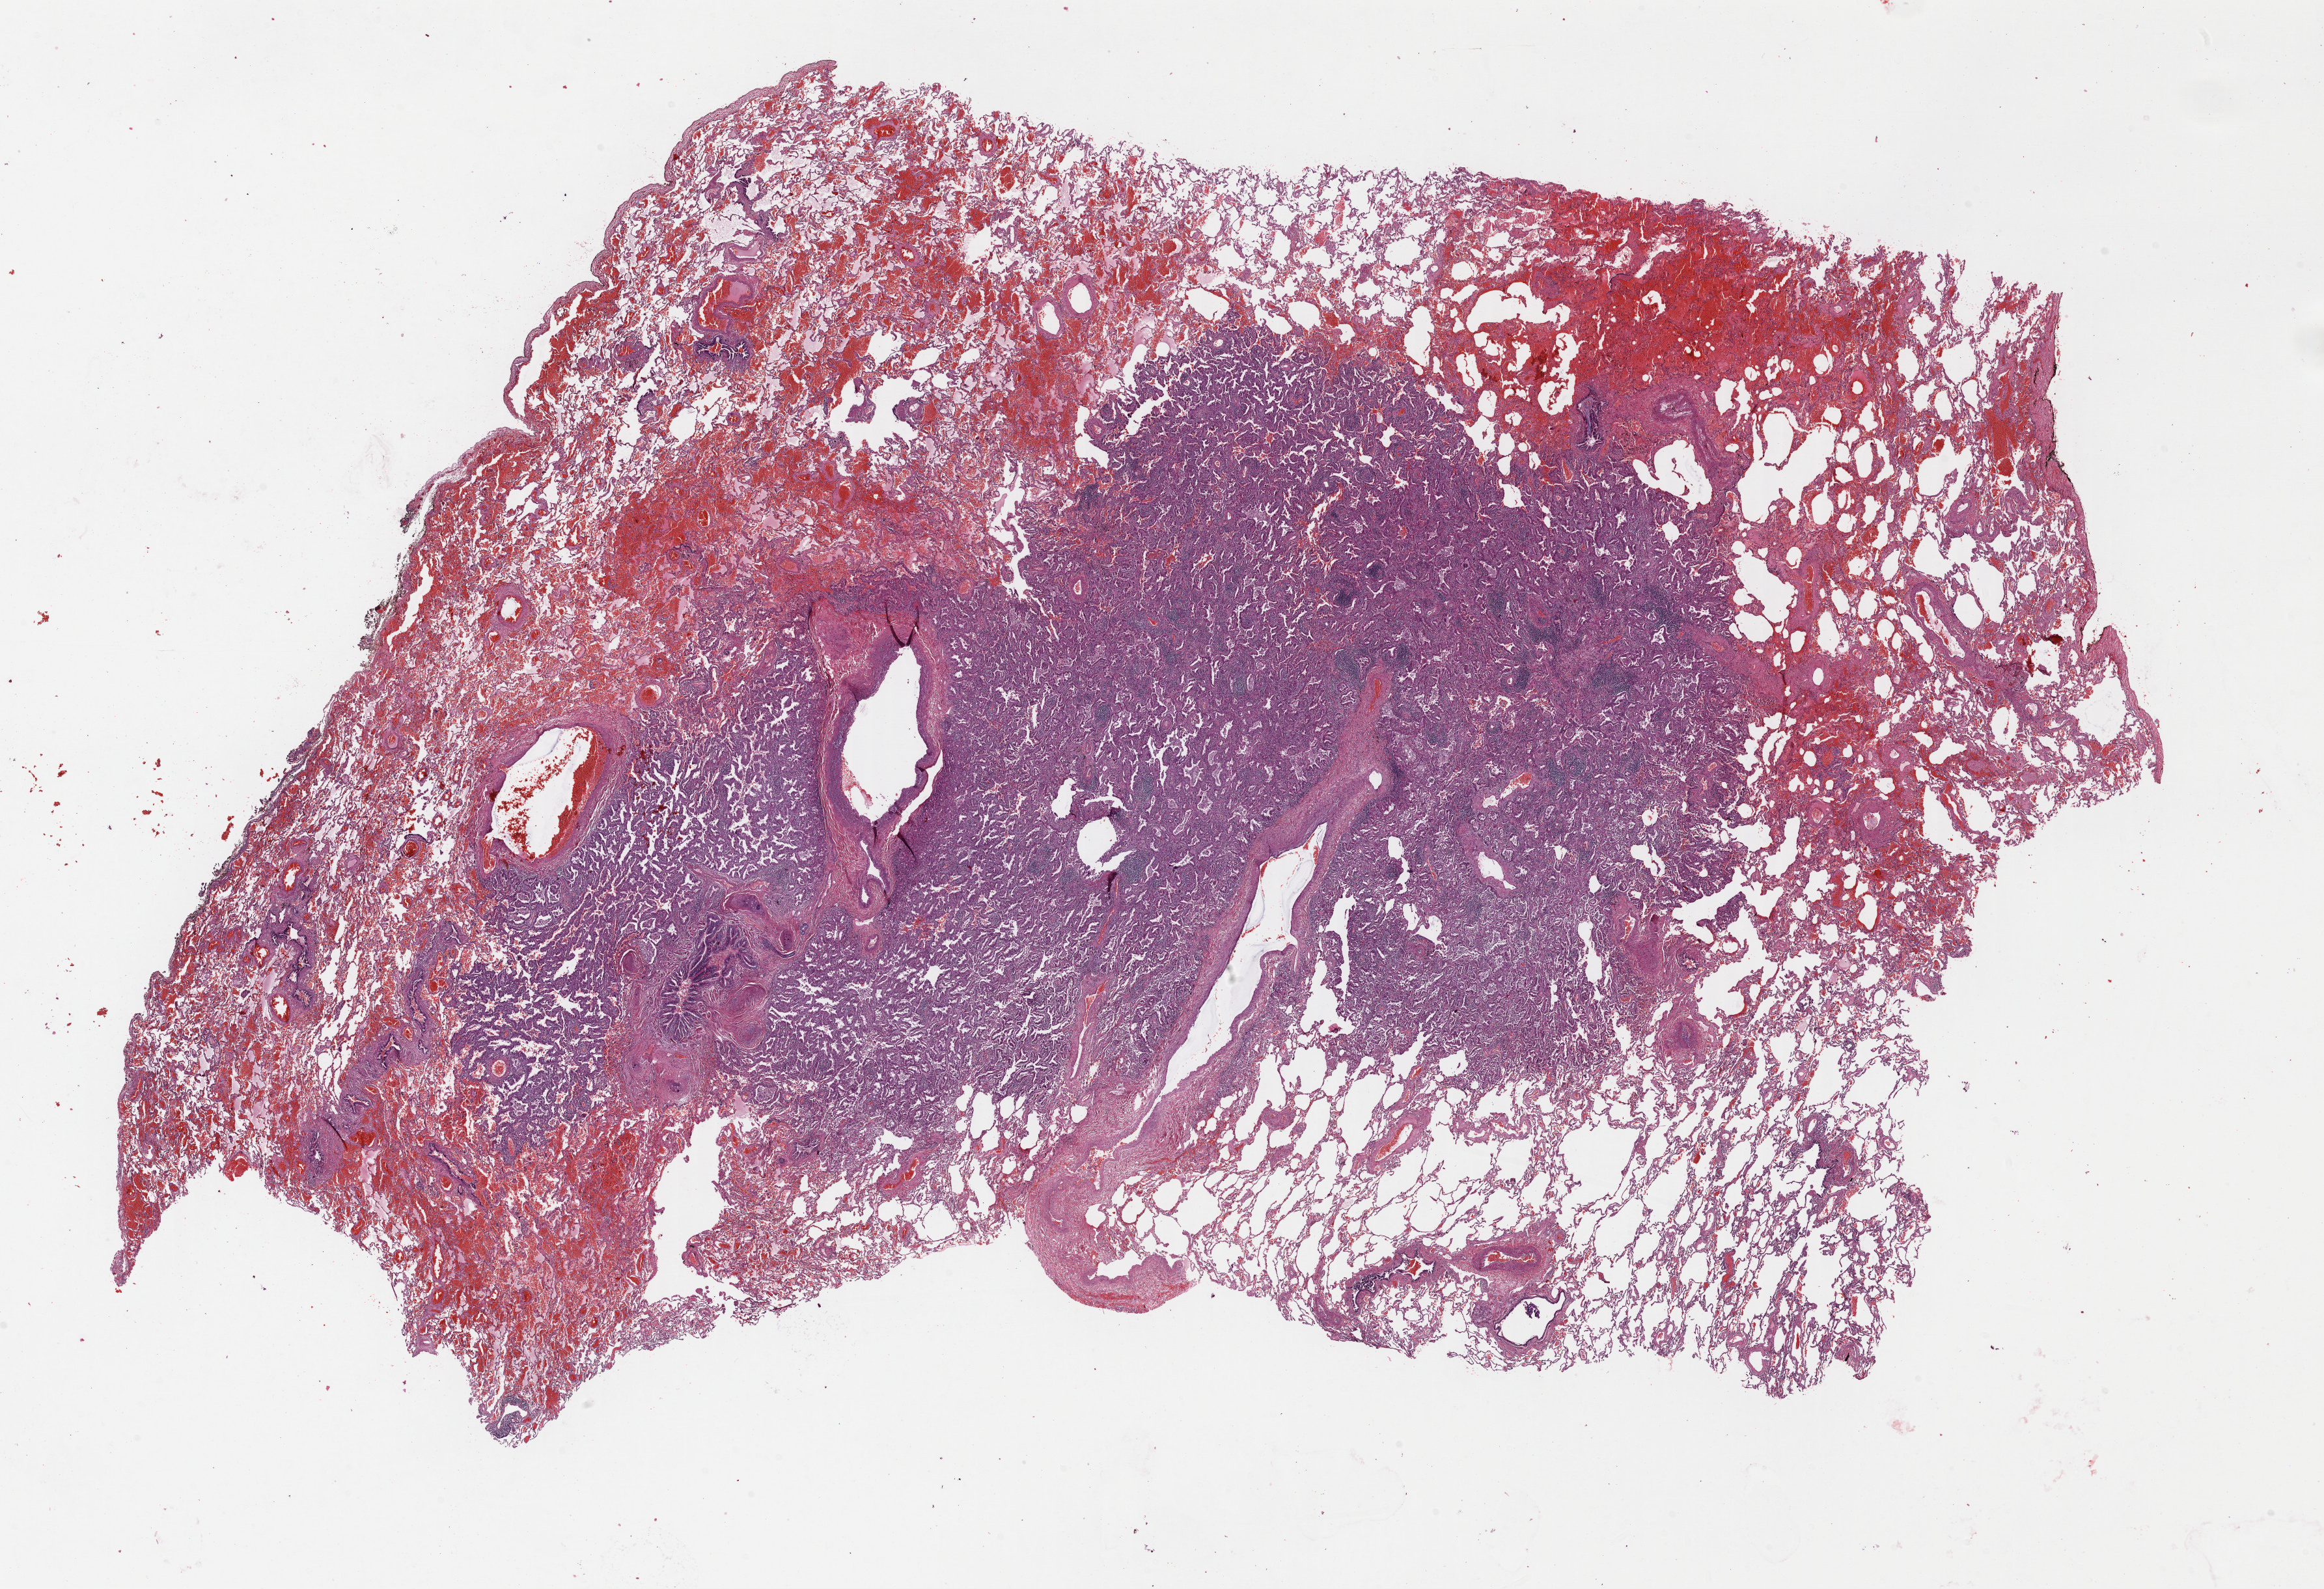
Hematoxylin and eosin (H&E) stained whole-slide image, a low-resolution overview of the entire scanned area, about 28.1 x 19.2 mm (from a 40x scan), formalin-fixed paraffin-embedded (FFPE) diagnostic section, sample: primary tumour, lung. Female patient; age at initial diagnosis 66 years.
* AJCC pathologic stage: IA
* histologic diagnosis: Adenocarcinoma, NOS (upper lobe, lung)